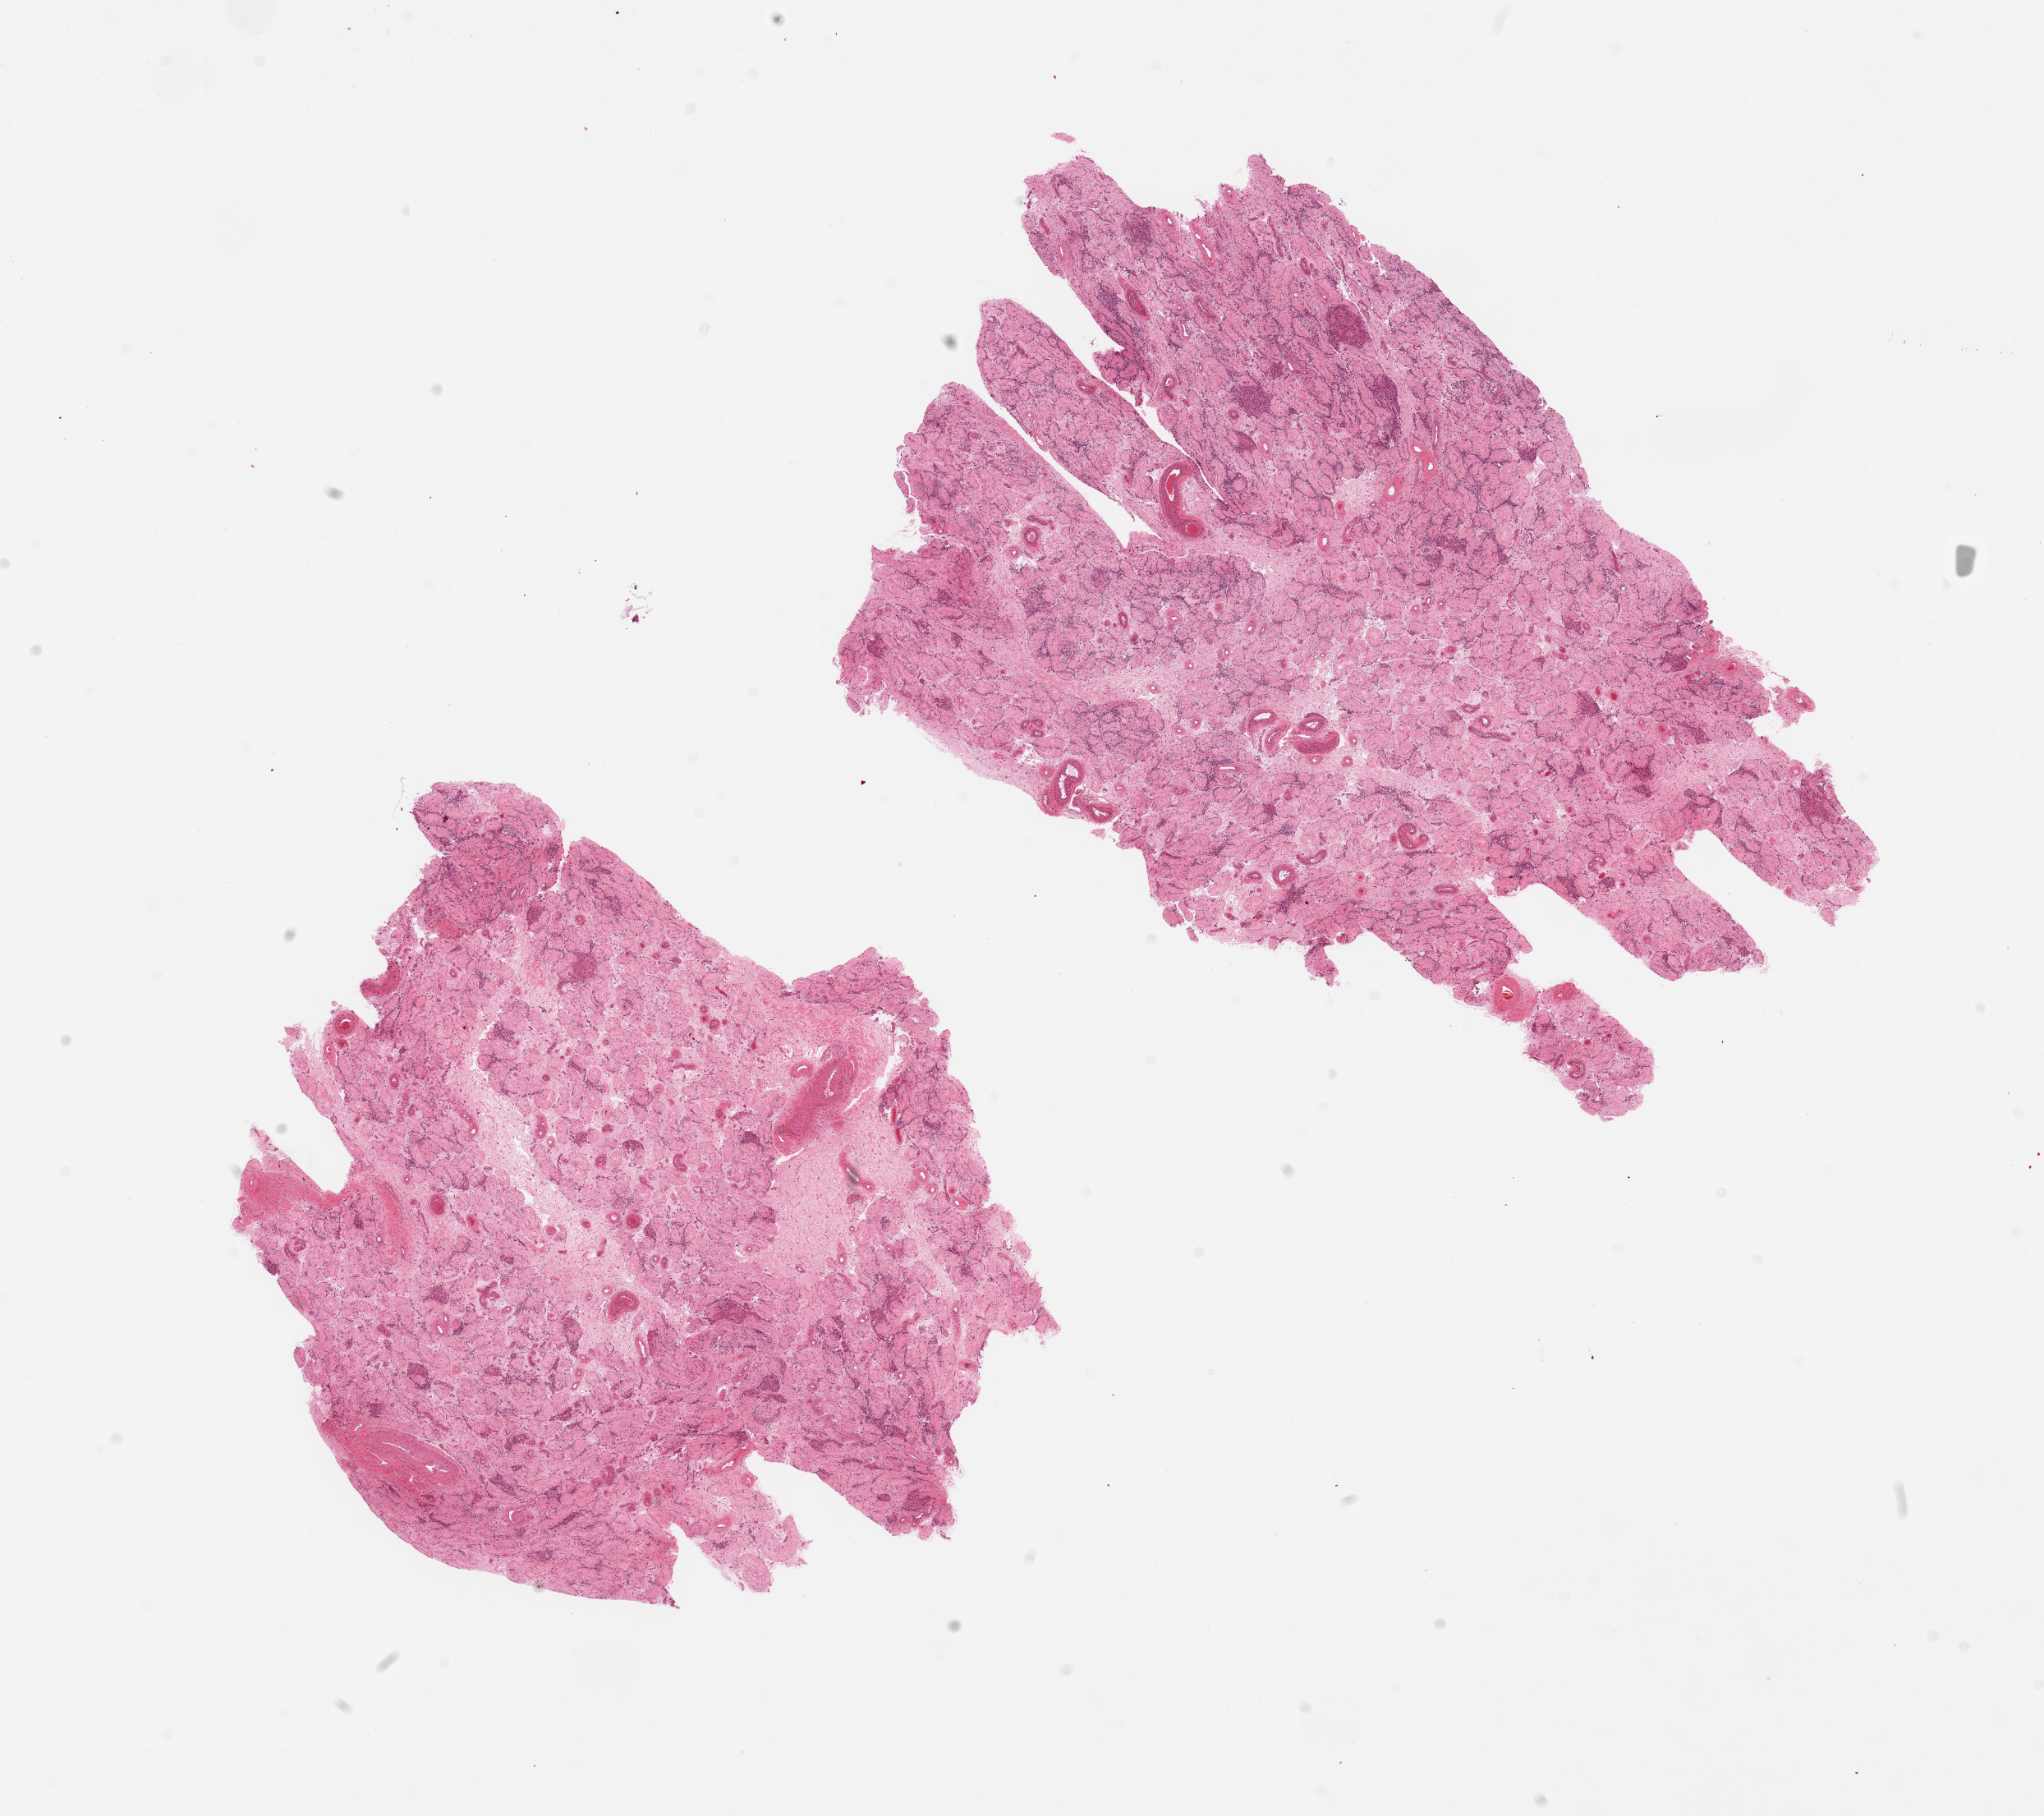
Whole-slide image, hematoxylin and eosin (H&E) stain, shown as a low-resolution overview of the whole scanned area (about 19.7 x 17.5 mm), PAXgene-fixed paraffin-embedded (PFPE) section, sampled site (target tissue): testis, tissue donor sample.
Pathologist's review note for this sample: 2 pieces, total seminiferous tubule atrophy/sclerosis with prominent Leydig cell hyperplasia.